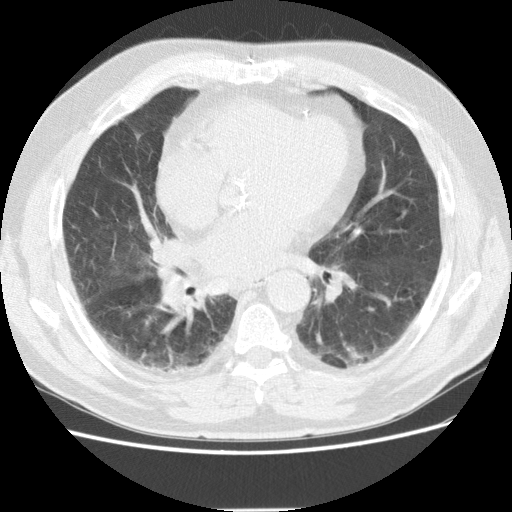
Low-dose screening chest CT, axial slice. Baseline annual screen. Lung window (W 1500 / L -600 HU). 2.5 mm slice thickness. Standard (soft-tissue) reconstruction kernel (STANDARD). 120 kVp. Slice 74 of 155 in the series. Male participant, aged 72 years at enrolment. Former smoker at enrolment.
Expert-annotated lung lesion, bounding box [x1, y1, x2, y2] px = [144, 229, 196, 268]. Screening reader's record for this exam: no non-calcified nodule ≥4 mm recorded. Lung cancer was diagnosed 163 days after this screen: adenocarcinoma, NOS, right middle lobe, stage IIIB (AJCC 6th edition), 27 mm at pathology.